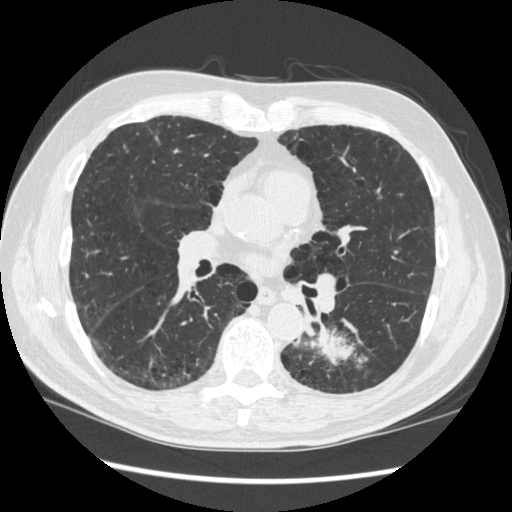
Low-dose screening chest CT, axial slice. First (baseline) screen. Lung window (W 1500 / L -600 HU). Standard (soft-tissue) reconstruction kernel (STANDARD). Slice 167 of 348 in the series. Male, age 72 years at enrolment. Current smoker at enrolment.
Lesion marked by an expert reader, bounding box (x1, y1, x2, y2) in pixels: (264, 306, 368, 399). The screening reader recorded 2 non-calcified nodules or masses ≥4 mm on this exam (left lower lobe, right middle lobe); which of them this box marks is not recorded. Lung cancer was diagnosed 37 days after this screen: squamous cell carcinoma, NOS, left lower lobe, stage IIIA (AJCC 6th edition), 60 mm at pathology.